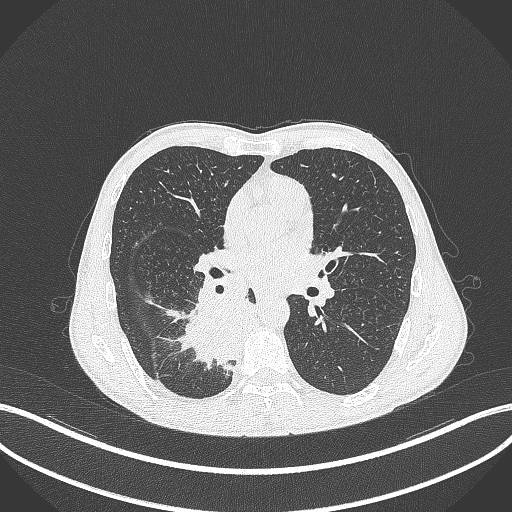
Chest CT, one axial slice; slice 194 of 371 in the series (ordered by position); reconstruction kernel B70f; 120 kVp; lung window (W 1500 / L -600 HU); 512 × 512 image matrix, field of view 400 × 400 mm. Patient: male, 58 years. Case-level facts recorded for this patient, not image findings: clinical TNM (as recorded): T3 N1 M1.
Outlined on this slice (rectangle marked by the reading radiologist):
- lung tumour (recorded histology: squamous cell carcinoma): bounding box (x1, y1, x2, y2) in pixels: (172, 282, 252, 365)